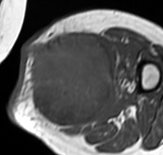
MRI of an extremity soft-tissue mass, one axial slice. Position 35 of 65 along the scan axis. MR volume resampled by the dataset authors to the PET/CT grid (not the native acquisition matrix). 3.27 mm slice thickness. 163 × 155 image matrix. Female patient. Case-level facts recorded for this patient, not image findings: histological type: pleomorphic leiomyosarcoma; grade: high; site of the primary tumour: left thigh.
Annotated regions visible in this slice (expert contour drawn on MRI and transferred to this co-registered scan by the dataset authors):
- gross tumour volume including surrounding oedema: bounding box [x1, y1, x2, y2] px = [26, 33, 120, 130]
- gross tumour volume (mass): [26, 33, 115, 130]